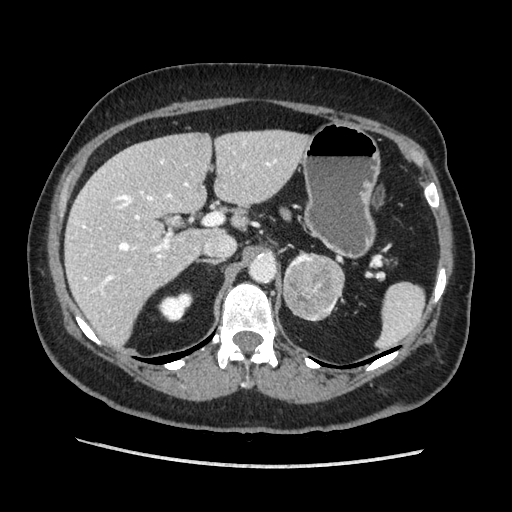
Contrast-enhanced abdominal CT, one axial slice; position 126 of 203 along the scan axis; soft-tissue window (W 400 / L 40 HU); 1.25 mm slice thickness; 512 × 512 image matrix. Female patient. Case-level facts recorded for this patient, not image findings: diagnosis: adrenocortical carcinoma; tumour side: left adrenal; tumour size at pathology: 6.5 cm; Ki-67 index: 22 %.
Structures marked on this image (semi-automatically segmented with operator editing):
- mass: bounding box (x1, y1, x2, y2) in pixels: (284, 251, 345, 321)